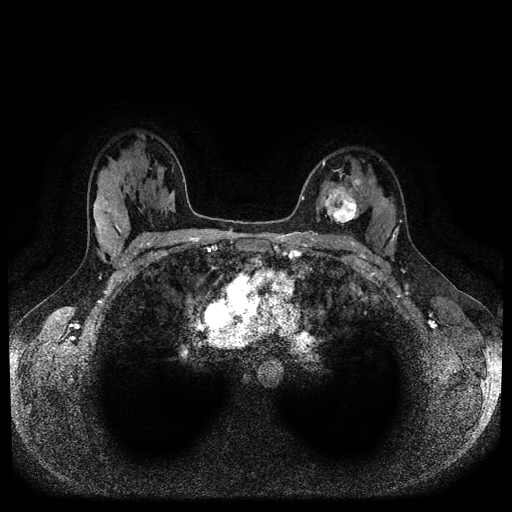
Breast MRI (dynamic contrast-enhanced, multi-phase), one axial slice. Slice 67 of 116 in the series (ordered by position). Dynamic contrast-enhanced series, time point 2 of 5 at this slice position (early post-contrast). 1.5 T. TE 2.6 ms, TR 5.3 ms. 2 mm slice thickness. 512 × 512 image matrix, field of view 350 × 350 mm. Female patient, age 33 years.
Structures marked on this image (semi-automatic segmentation, software-assisted and operator-edited):
- breast lesion (labelled 'tumour' in the annotation; benign lesions carry a separate 'benign' label): bounding box [x1, y1, x2, y2] px = [323, 183, 360, 226]